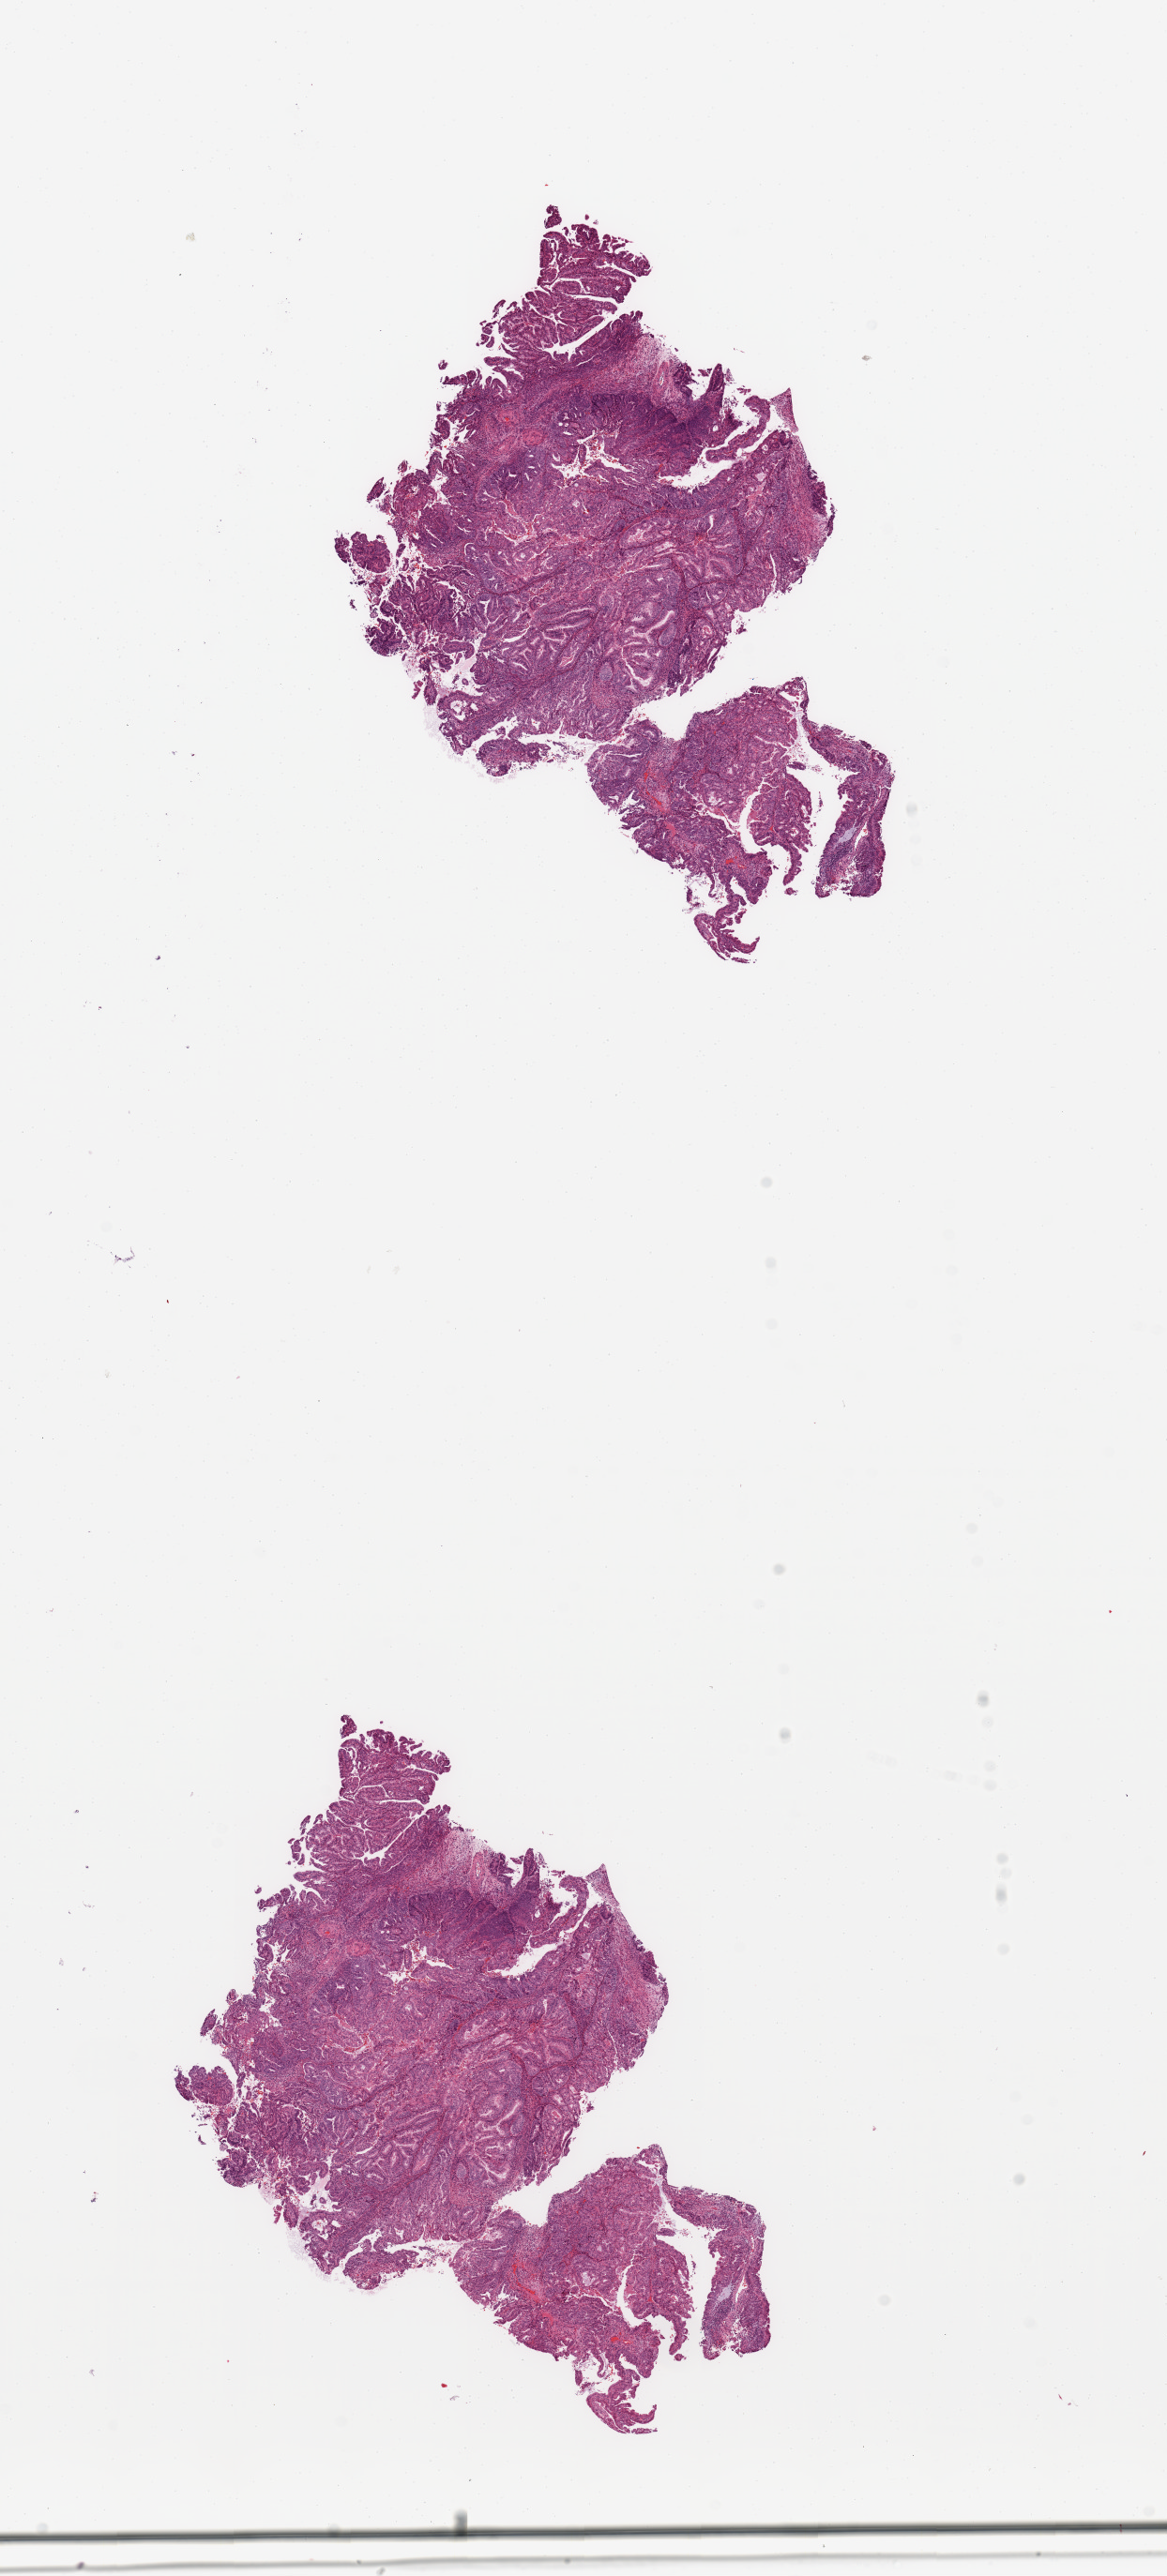
Whole-slide histology image, H&E-stained — shown as a low-resolution overview of the whole scanned area (about 9.8 x 21.7 mm, acquisition: 20x scan); tumour tissue sample, sampled site: uterus. 59-year-old female patient. Histologic grade: G2 (moderately differentiated). Composition of this section per pathologist review: tumour nuclei 90%, necrosis 5%.
- histologic diagnosis: Endometrioid adenocarcinoma, NOS
- AJCC pathologic stage: I